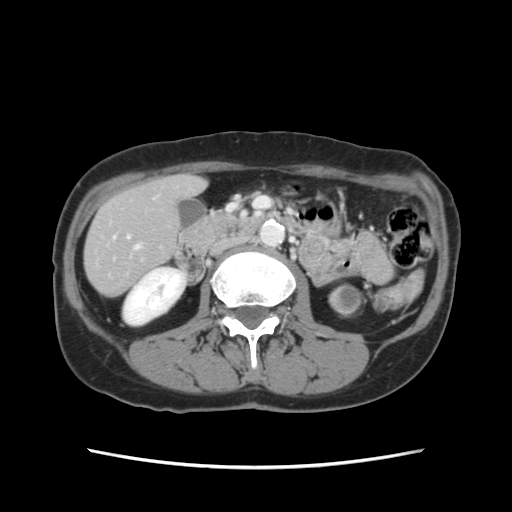
Contrast-enhanced abdominal CT, one axial slice; slice 38 of 120 in the series (ordered by position); 120 kVp; intravenous contrast given; soft-tissue window (W 400 / L 40 HU); 2.5 mm slice thickness; 512 × 512 image matrix, field of view 330 × 330 mm. Female patient, age 70 years. From the clinical record (not read from this slice): diagnosis: colorectal cancer liver metastases, imaged before liver resection.
Annotated regions visible in this slice (manually delineated by an expert):
- hepatic veins: bounding box (x1, y1, x2, y2) in pixels: (135, 245, 140, 249)
- liver: (85, 176, 204, 295)
- planned liver remnant (the part of the liver to remain after resection): (84, 176, 204, 295)
- portal vein (with intrahepatic branches): (127, 236, 130, 239)